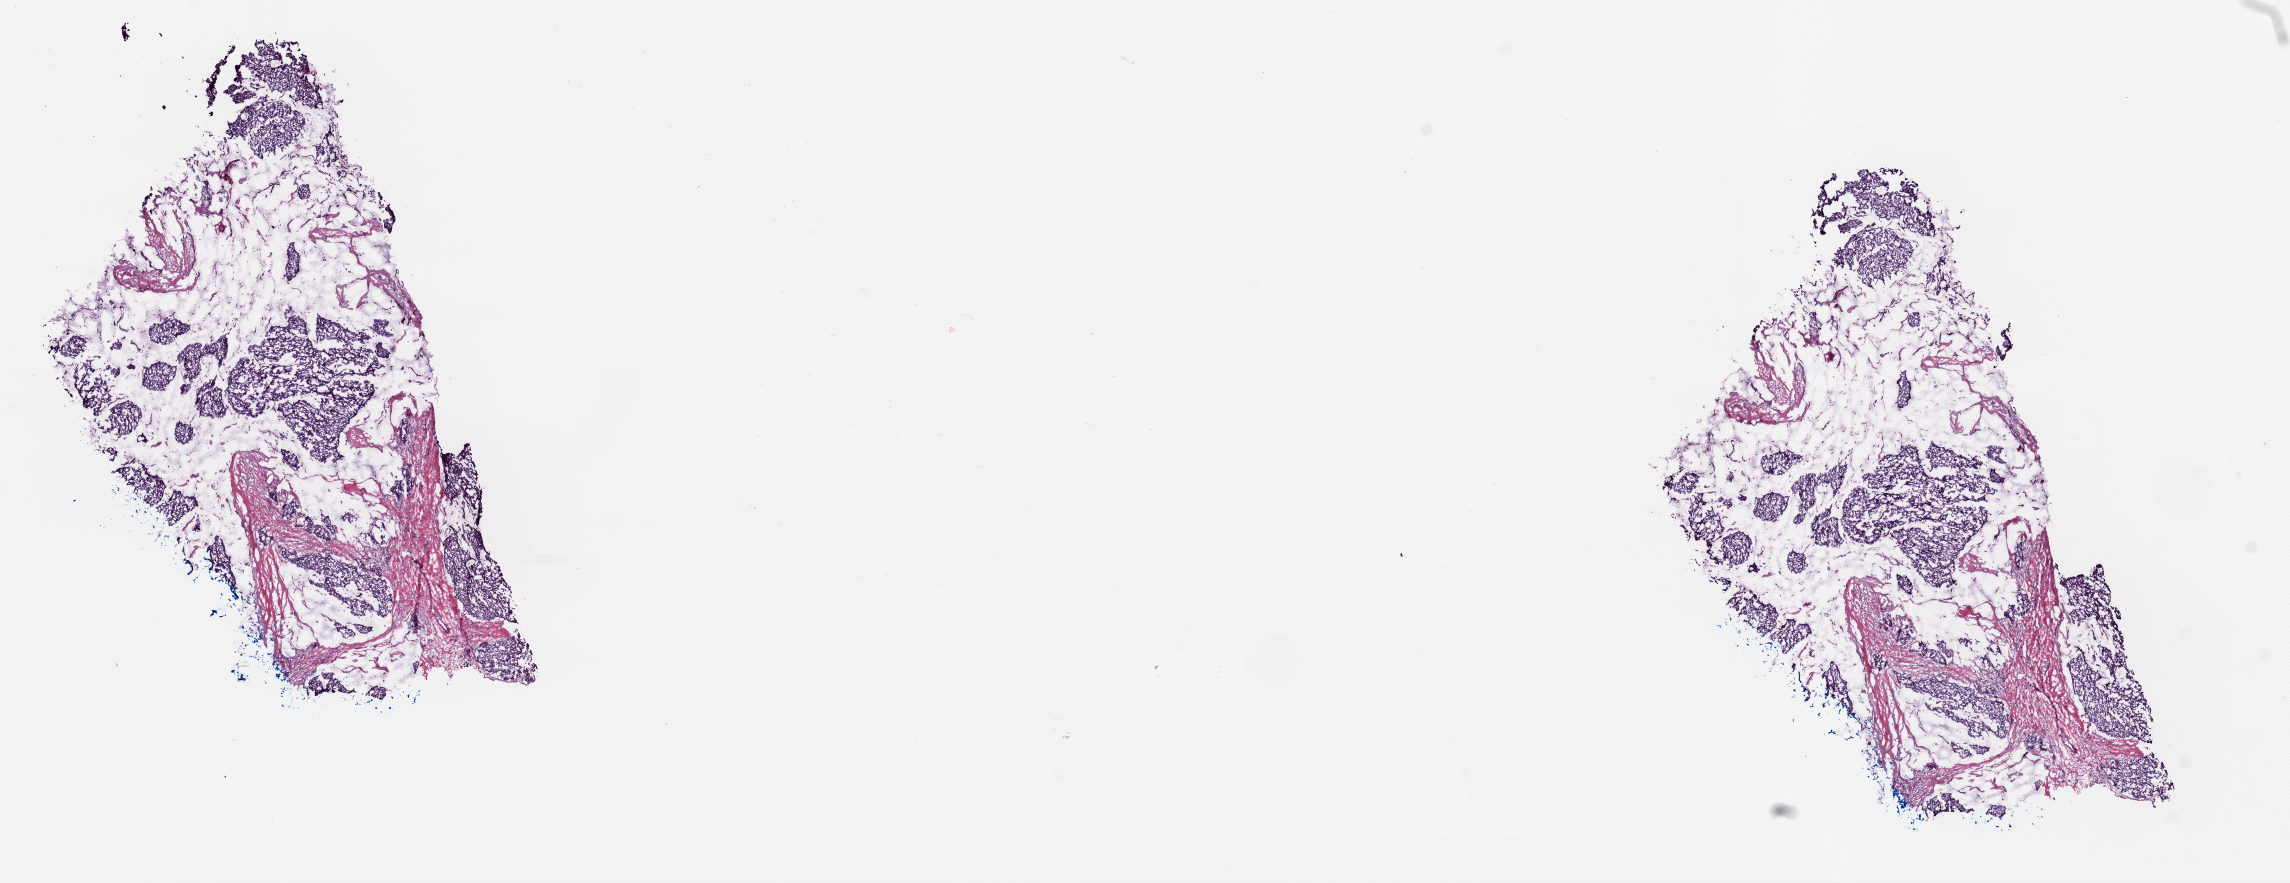
Digitized Hematoxylin and eosin (H&E) stained tissue section (whole slide), shown as a low-resolution overview of the whole scanned area (about 18.1 x 7.0 mm). Frozen section from the top of the tissue portion. Sample: primary tumour, breast. Female patient; age at initial diagnosis 66 years. Pathologist review of this section (percent, as recorded): tumour cells 90%, tumour nuclei 85%, normal cells 0%, stromal cells 10%, necrosis 0%. Infiltration values recorded for this section: lymphocyte infiltration 0%, monocyte infiltration 0%, neutrophil infiltration 0%.
Laterality: left. Lymph nodes positive (case pathology): 0 of 1 examined. AJCC pathologic stage: IA. Pathologic diagnosis: Infiltrating duct mixed with other types of carcinoma.